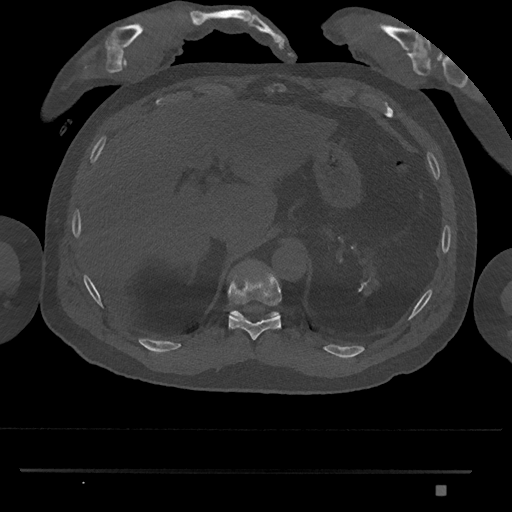
CT including the spine, one axial slice; position 990 of 1134 along the scan axis; bone window (W 1800 / L 400 HU); 0.5 mm slice thickness; 512 × 512 image matrix. Patient: male, 65 years. From the clinical record (not read from this slice): primary cancer: prostate.
Annotated regions visible in this slice (semi-automatic segmentation, software-assisted and operator-edited):
- T10 vertebra: bounding box <228,266,282,341> (left, top, right, bottom; pixels)
- T11 vertebra: <230,309,279,319>